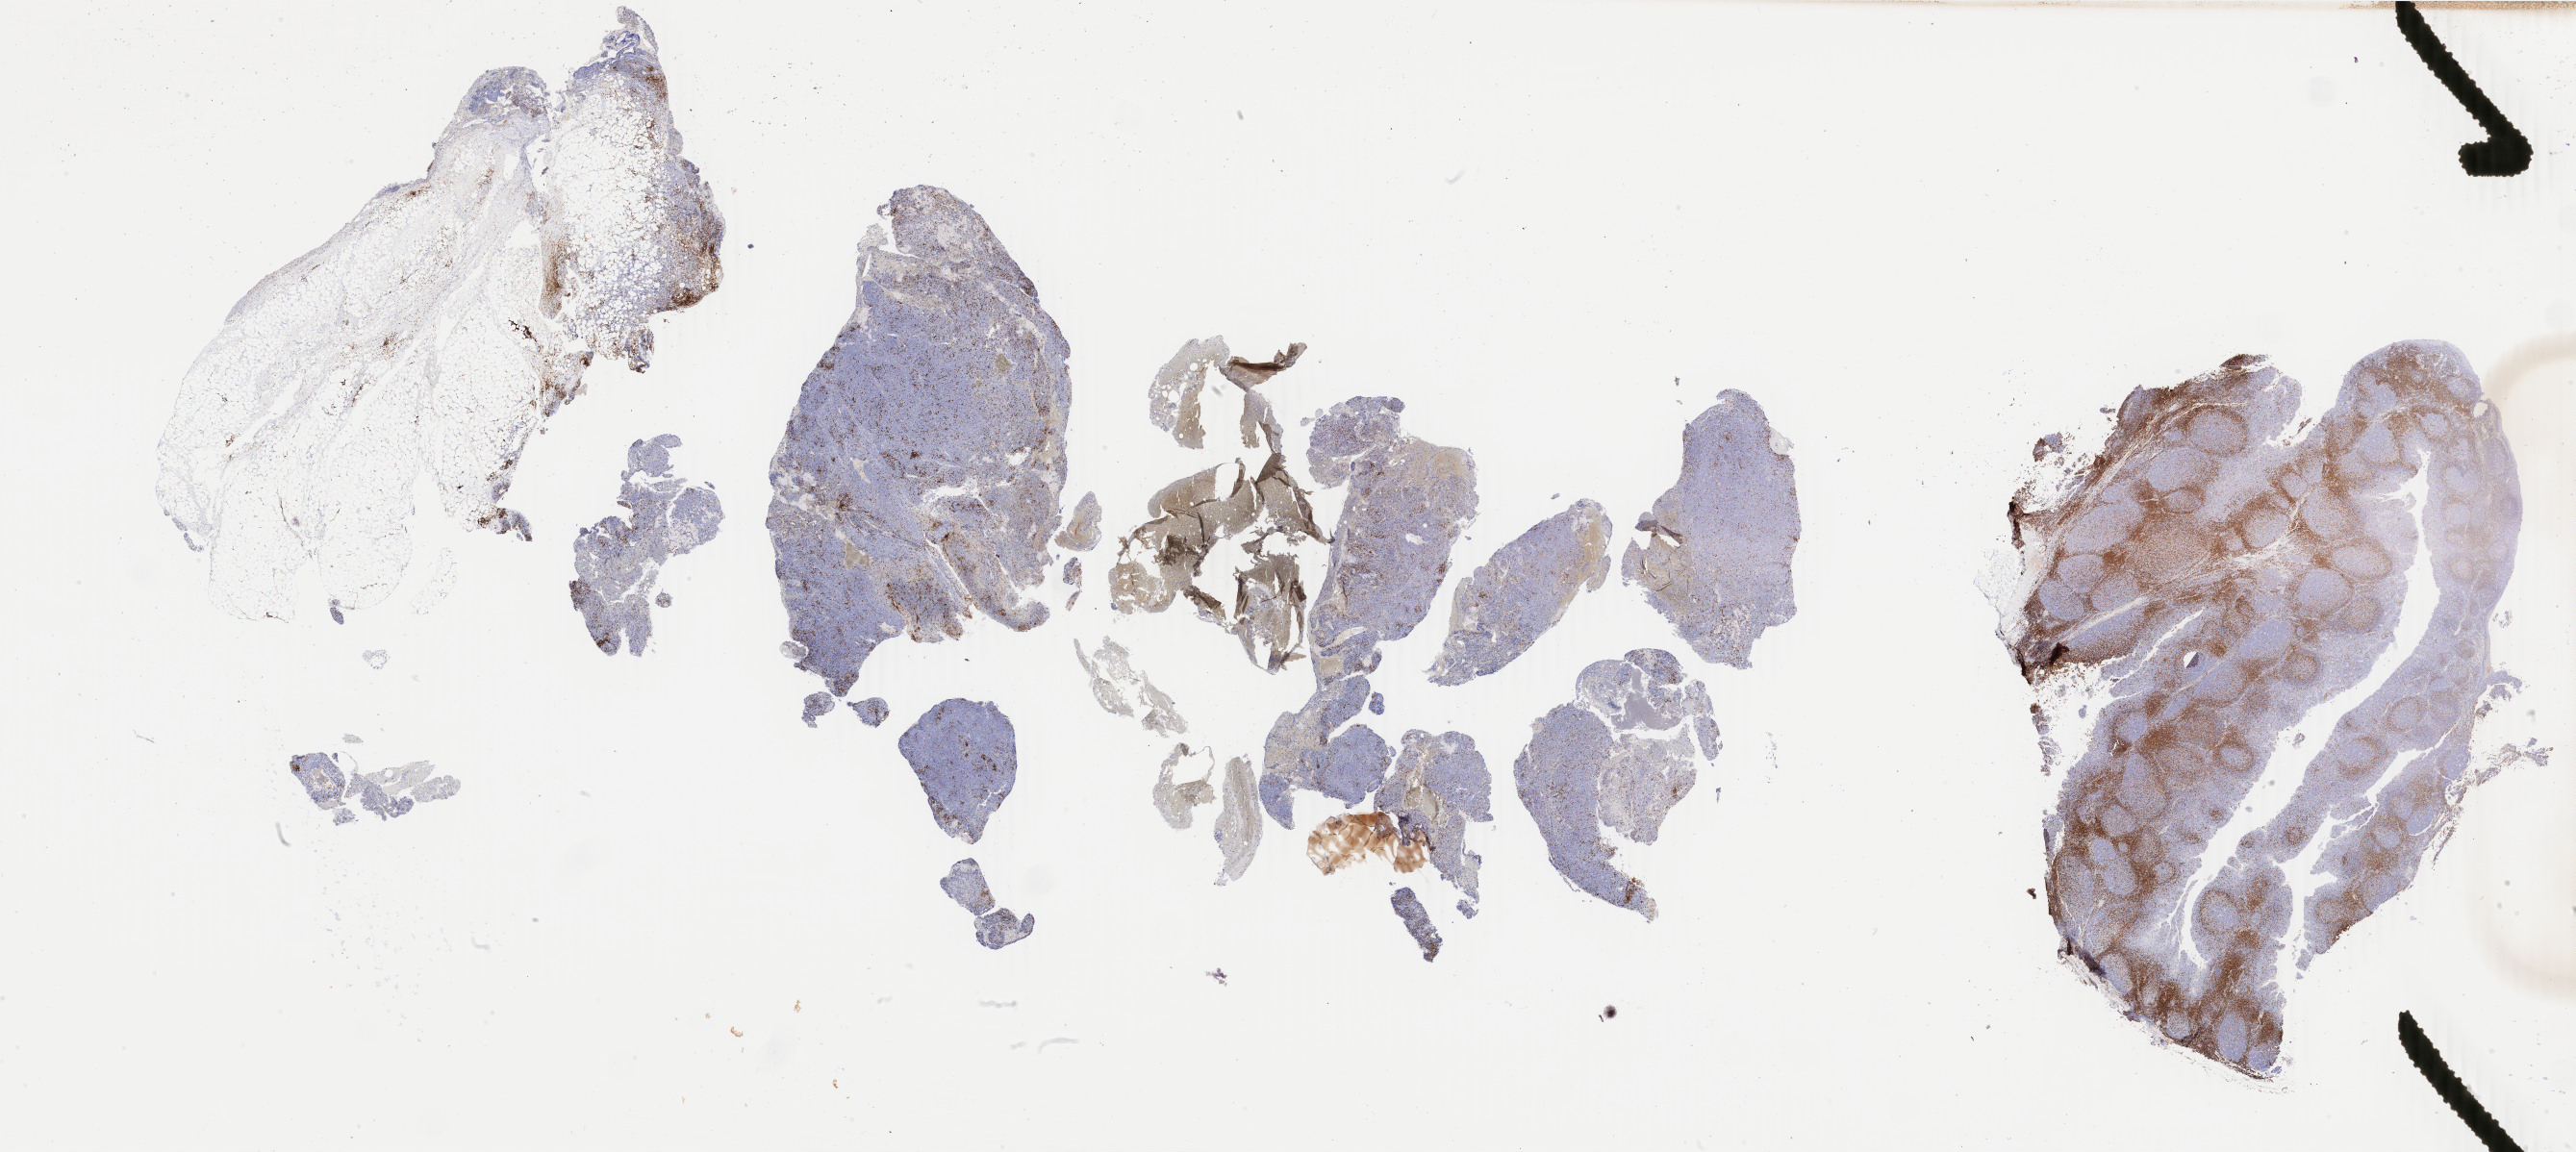
Immunohistochemistry (IHC) whole-slide image stained for CD3, shown as a low-resolution overview of the whole scanned area (about 42.6 x 19.1 mm). Tumor tissue. Site: abdominal lymph node. Patient: male, age 27 years.
Diagnosis: Burkitt lymphoma, NOS.